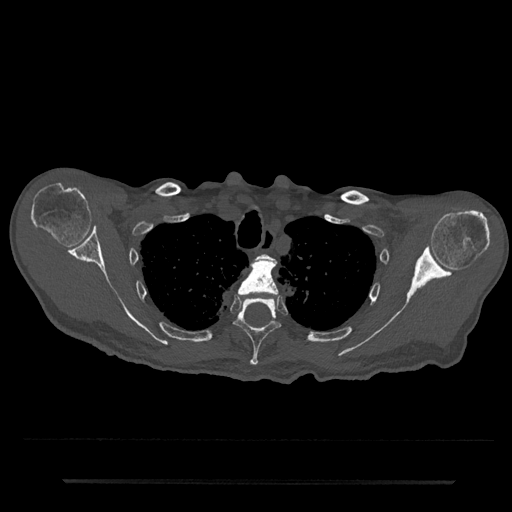
CT including the spine, one axial slice; slice 630 of 797 in the series (ordered by position); reconstruction kernel Br40s/3; bone window (W 1800 / L 400 HU); 0.5 mm slice thickness; 512 × 512 image matrix. Male patient, age 74 years. Case-level facts recorded for this patient, not image findings: primary cancer: prostate.
Structures marked on this image (semi-automatically segmented with operator editing):
- T2 vertebra: bounding box <258,254,272,260> (left, top, right, bottom; pixels)
- T3 vertebra: <238,257,279,295>
- T4 vertebra: <234,299,281,366>